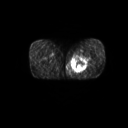
FDG PET of an extremity soft-tissue mass (from a PET/CT study), one axial slice. Position 20 of 267 along the scan axis. 3.27 mm slice thickness. 128 × 128 image matrix, field of view 600 × 600 mm. Patient: male, 59 years. From the clinical record (not read from this slice): histological type: pleiomorphic liposarcoma; grade: high; site of the primary tumour: left thigh.
Outlined on this slice (expert contour drawn on MRI and transferred to this co-registered scan by the dataset authors):
- gross tumour volume including surrounding oedema: box from (x=71, y=54) to (x=91, y=74) px
- gross tumour volume (mass): (x=72, y=56)–(x=87, y=73)